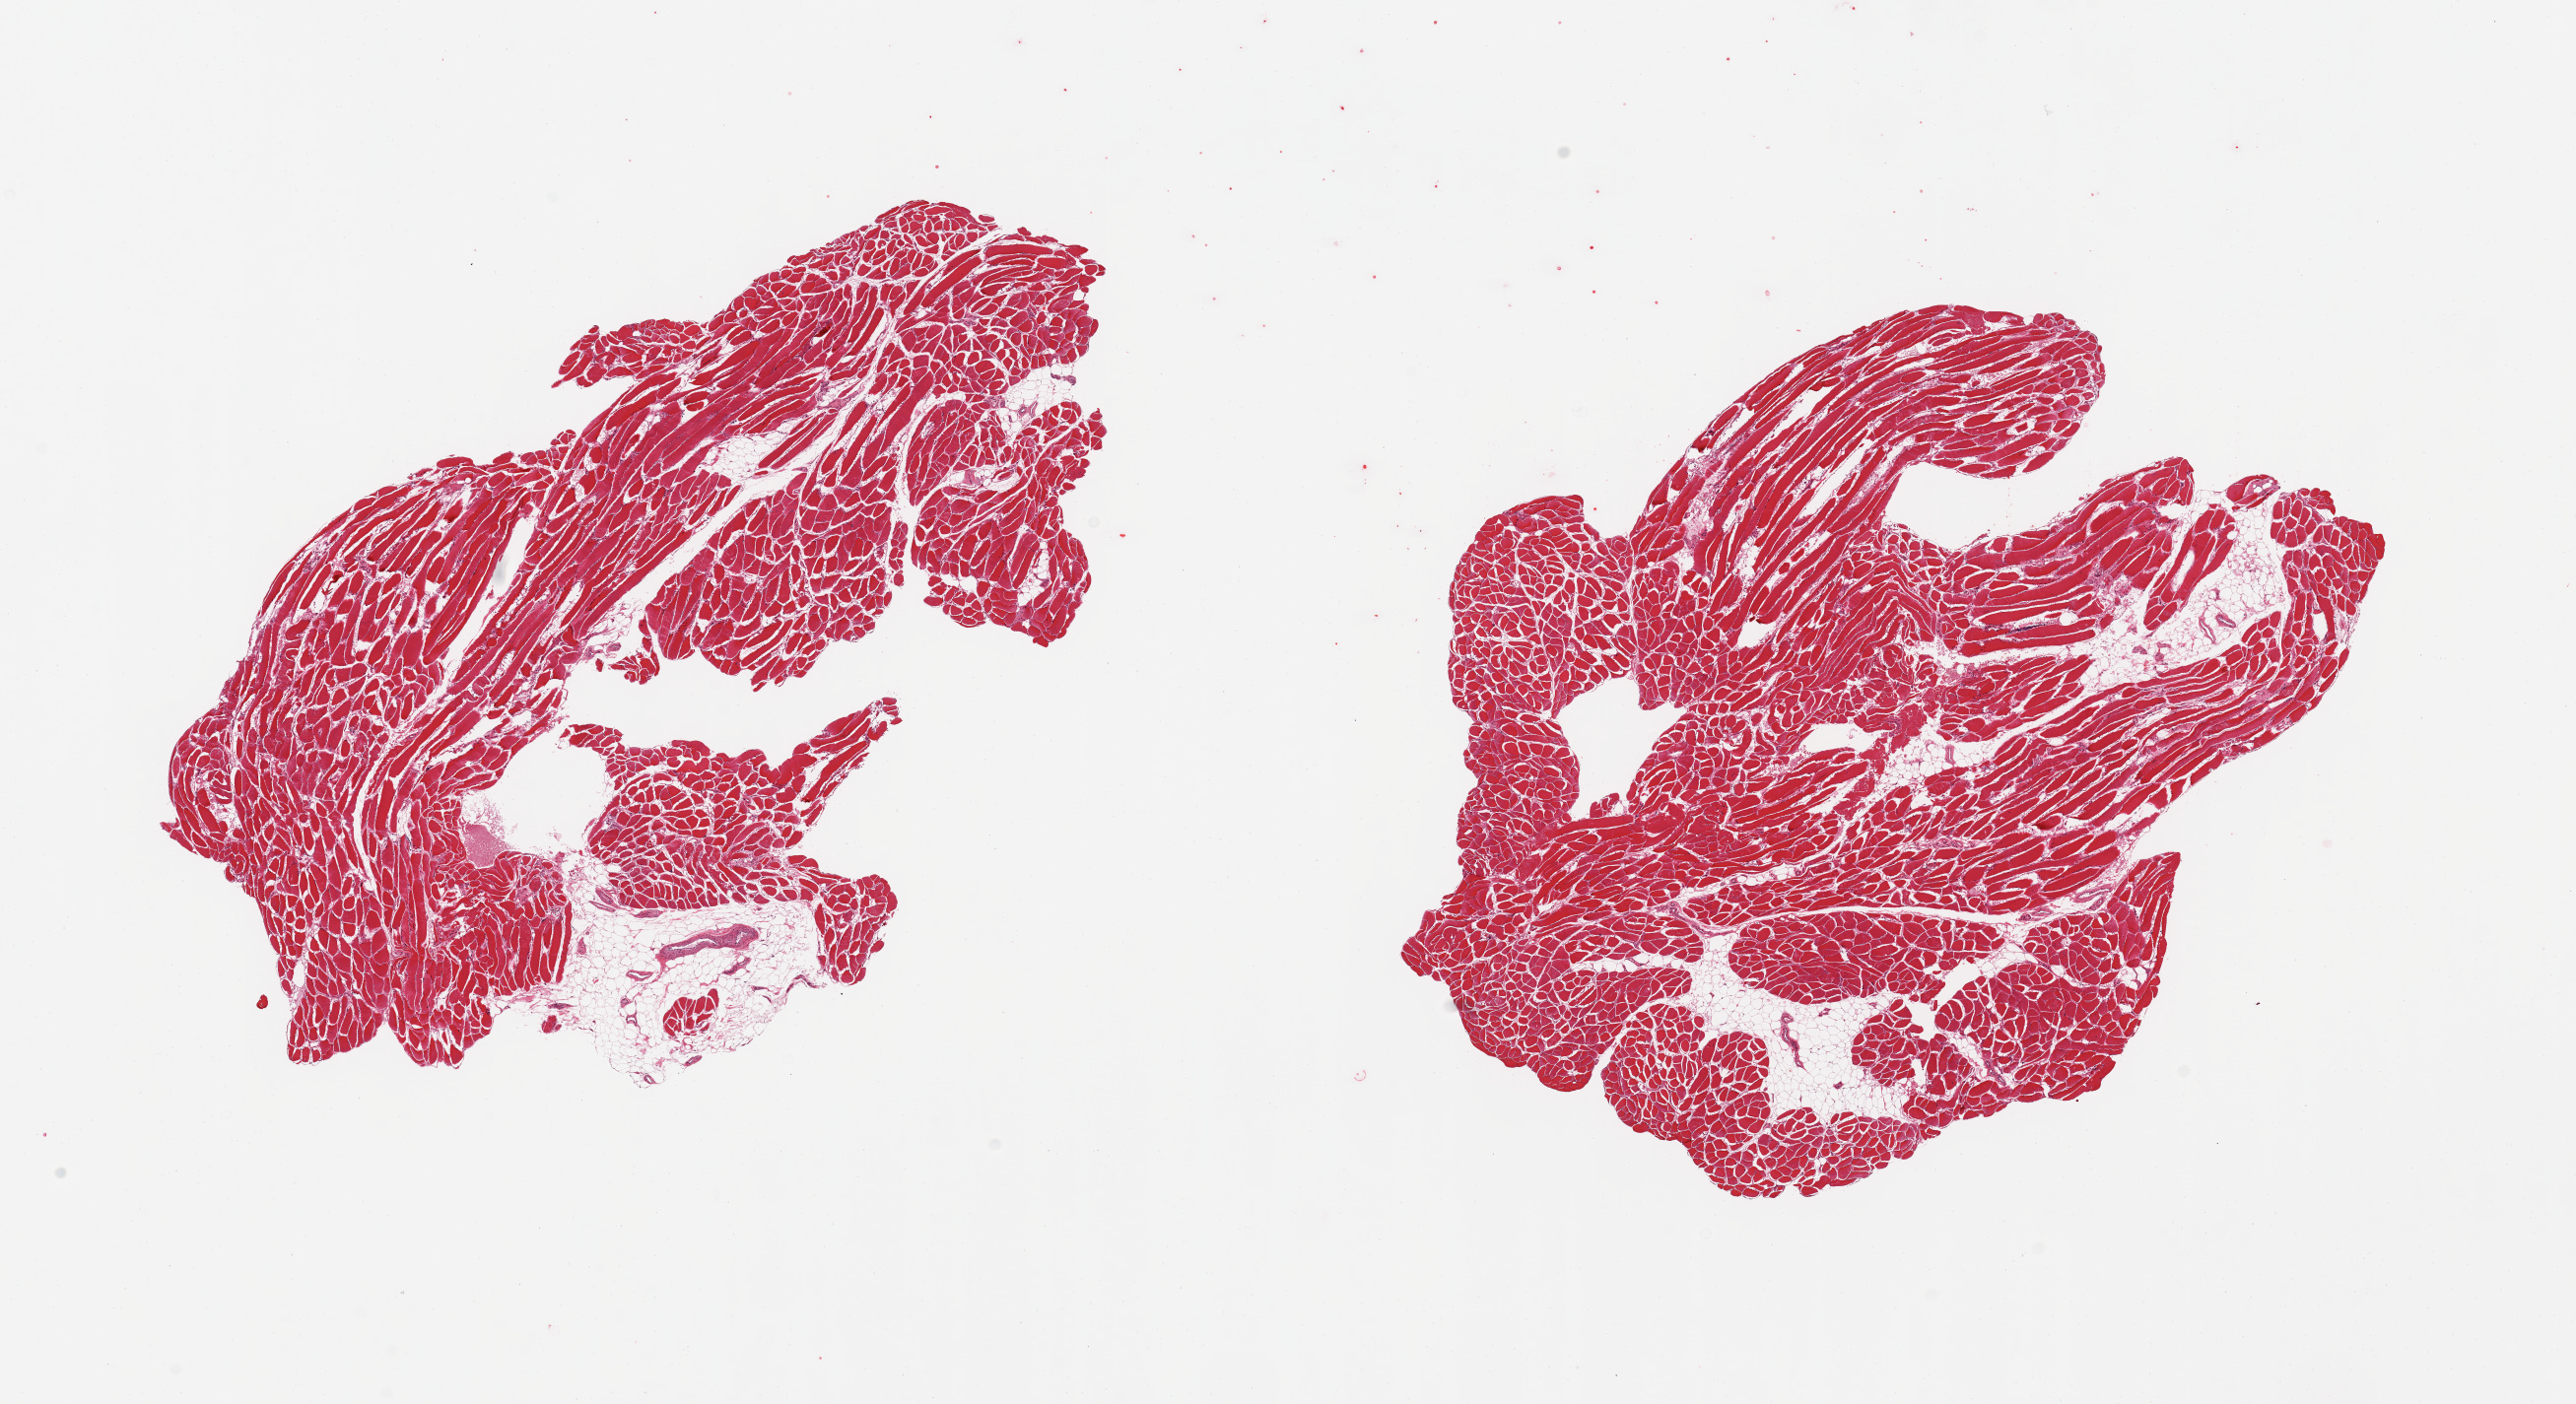
Whole-slide image, haematoxylin and eosin stain, brightfield — whole scanned area (about 20.7 x 11.3 mm, acquisition: 20x scan) shown as a low-resolution overview, PAXgene-fixed, paraffin-embedded tissue, target tissue: skeletal muscle, tissue donor sample. Female donor.
- pathologist's review note for this sample: 2 pieces; 10% fat content